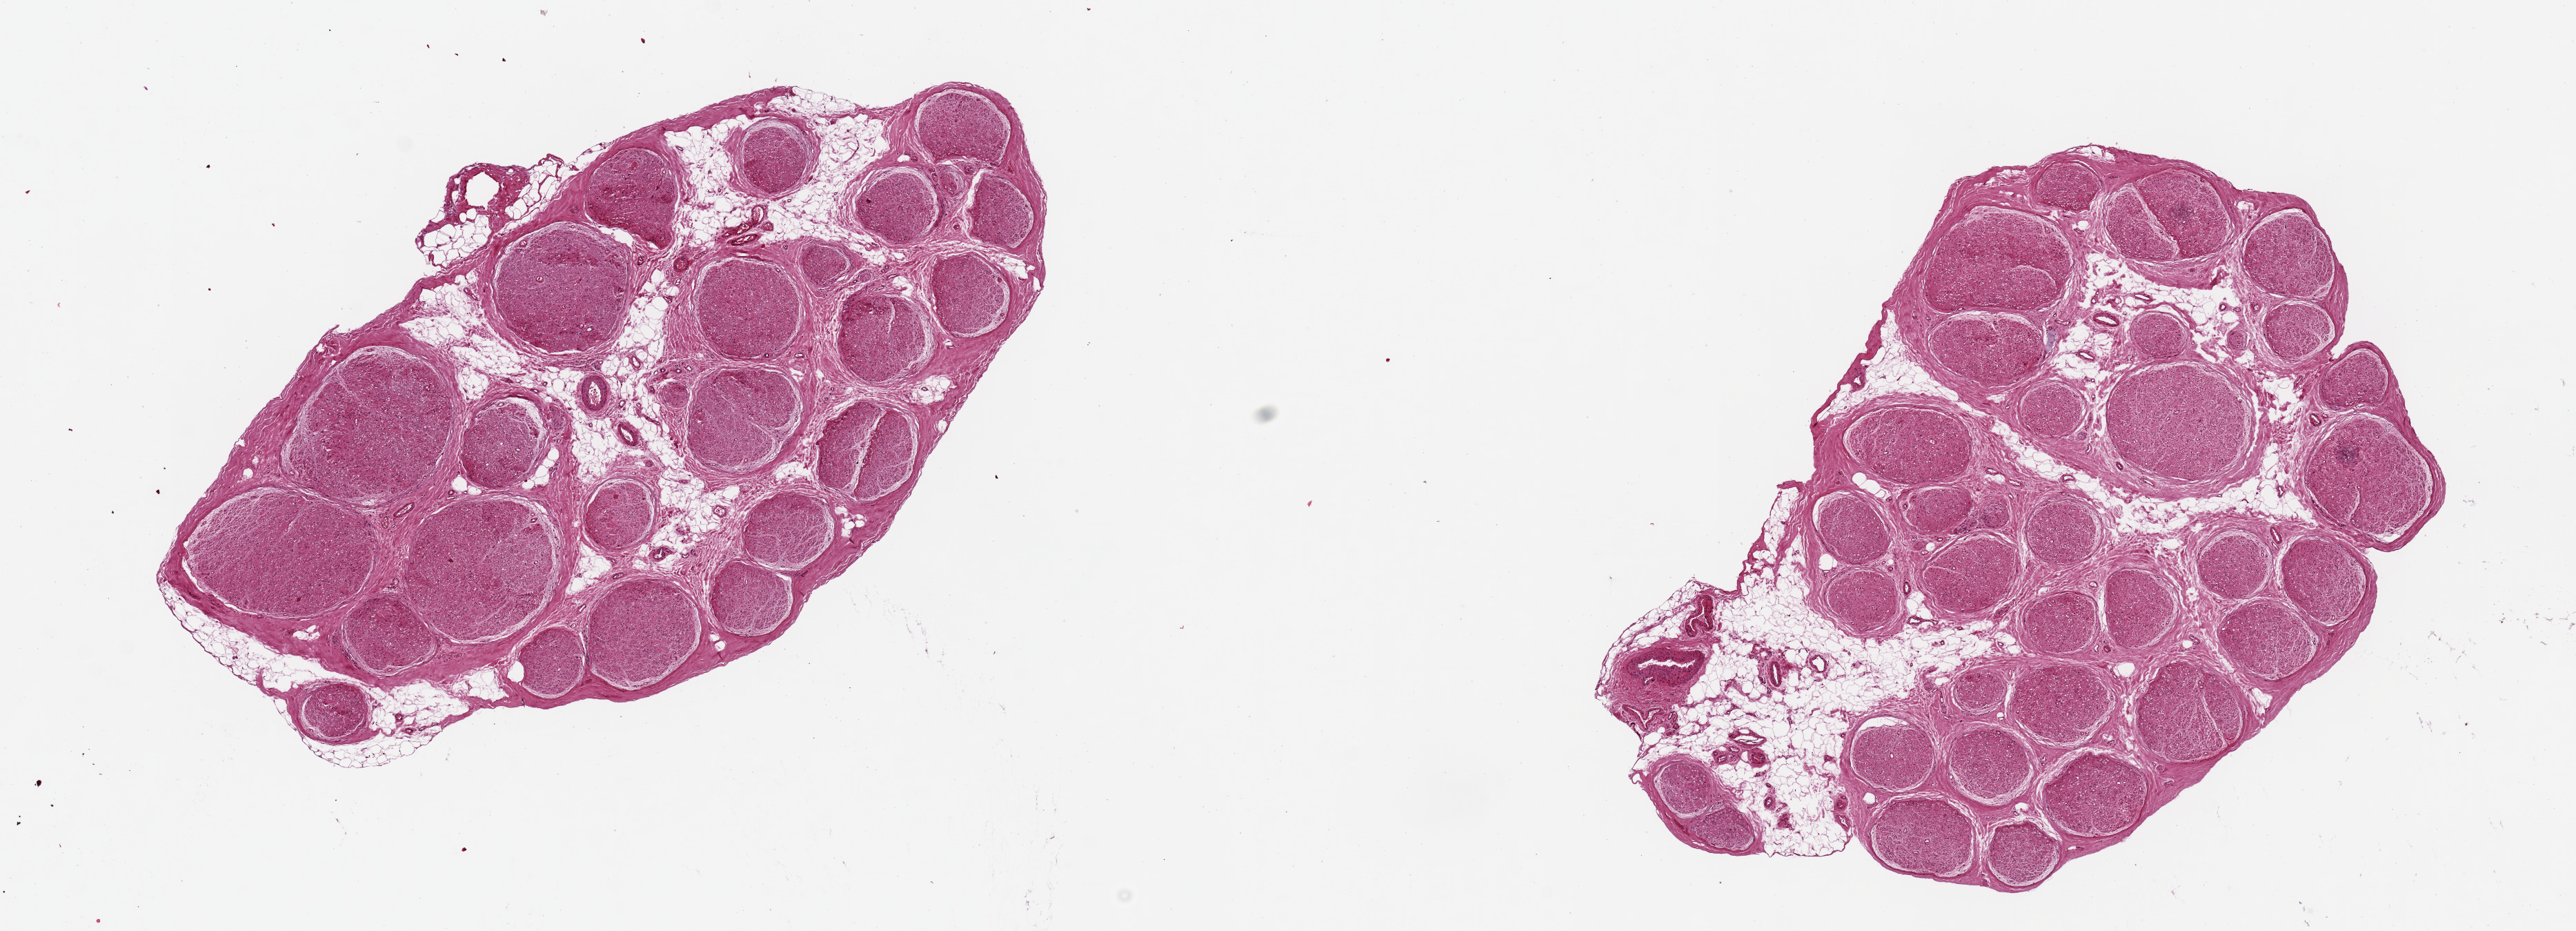
Whole-slide image, H&E stain, a low-resolution overview of the entire scanned area, about 14.8 x 5.3 mm, PAXgene-fixed paraffin-embedded (PFPE) section, section of tibial nerve (target tissue), donor tissue sample. Male donor.
- pathologist's review note for this sample: 2 aliquots, ~4.5x3mm. Good clean specimens